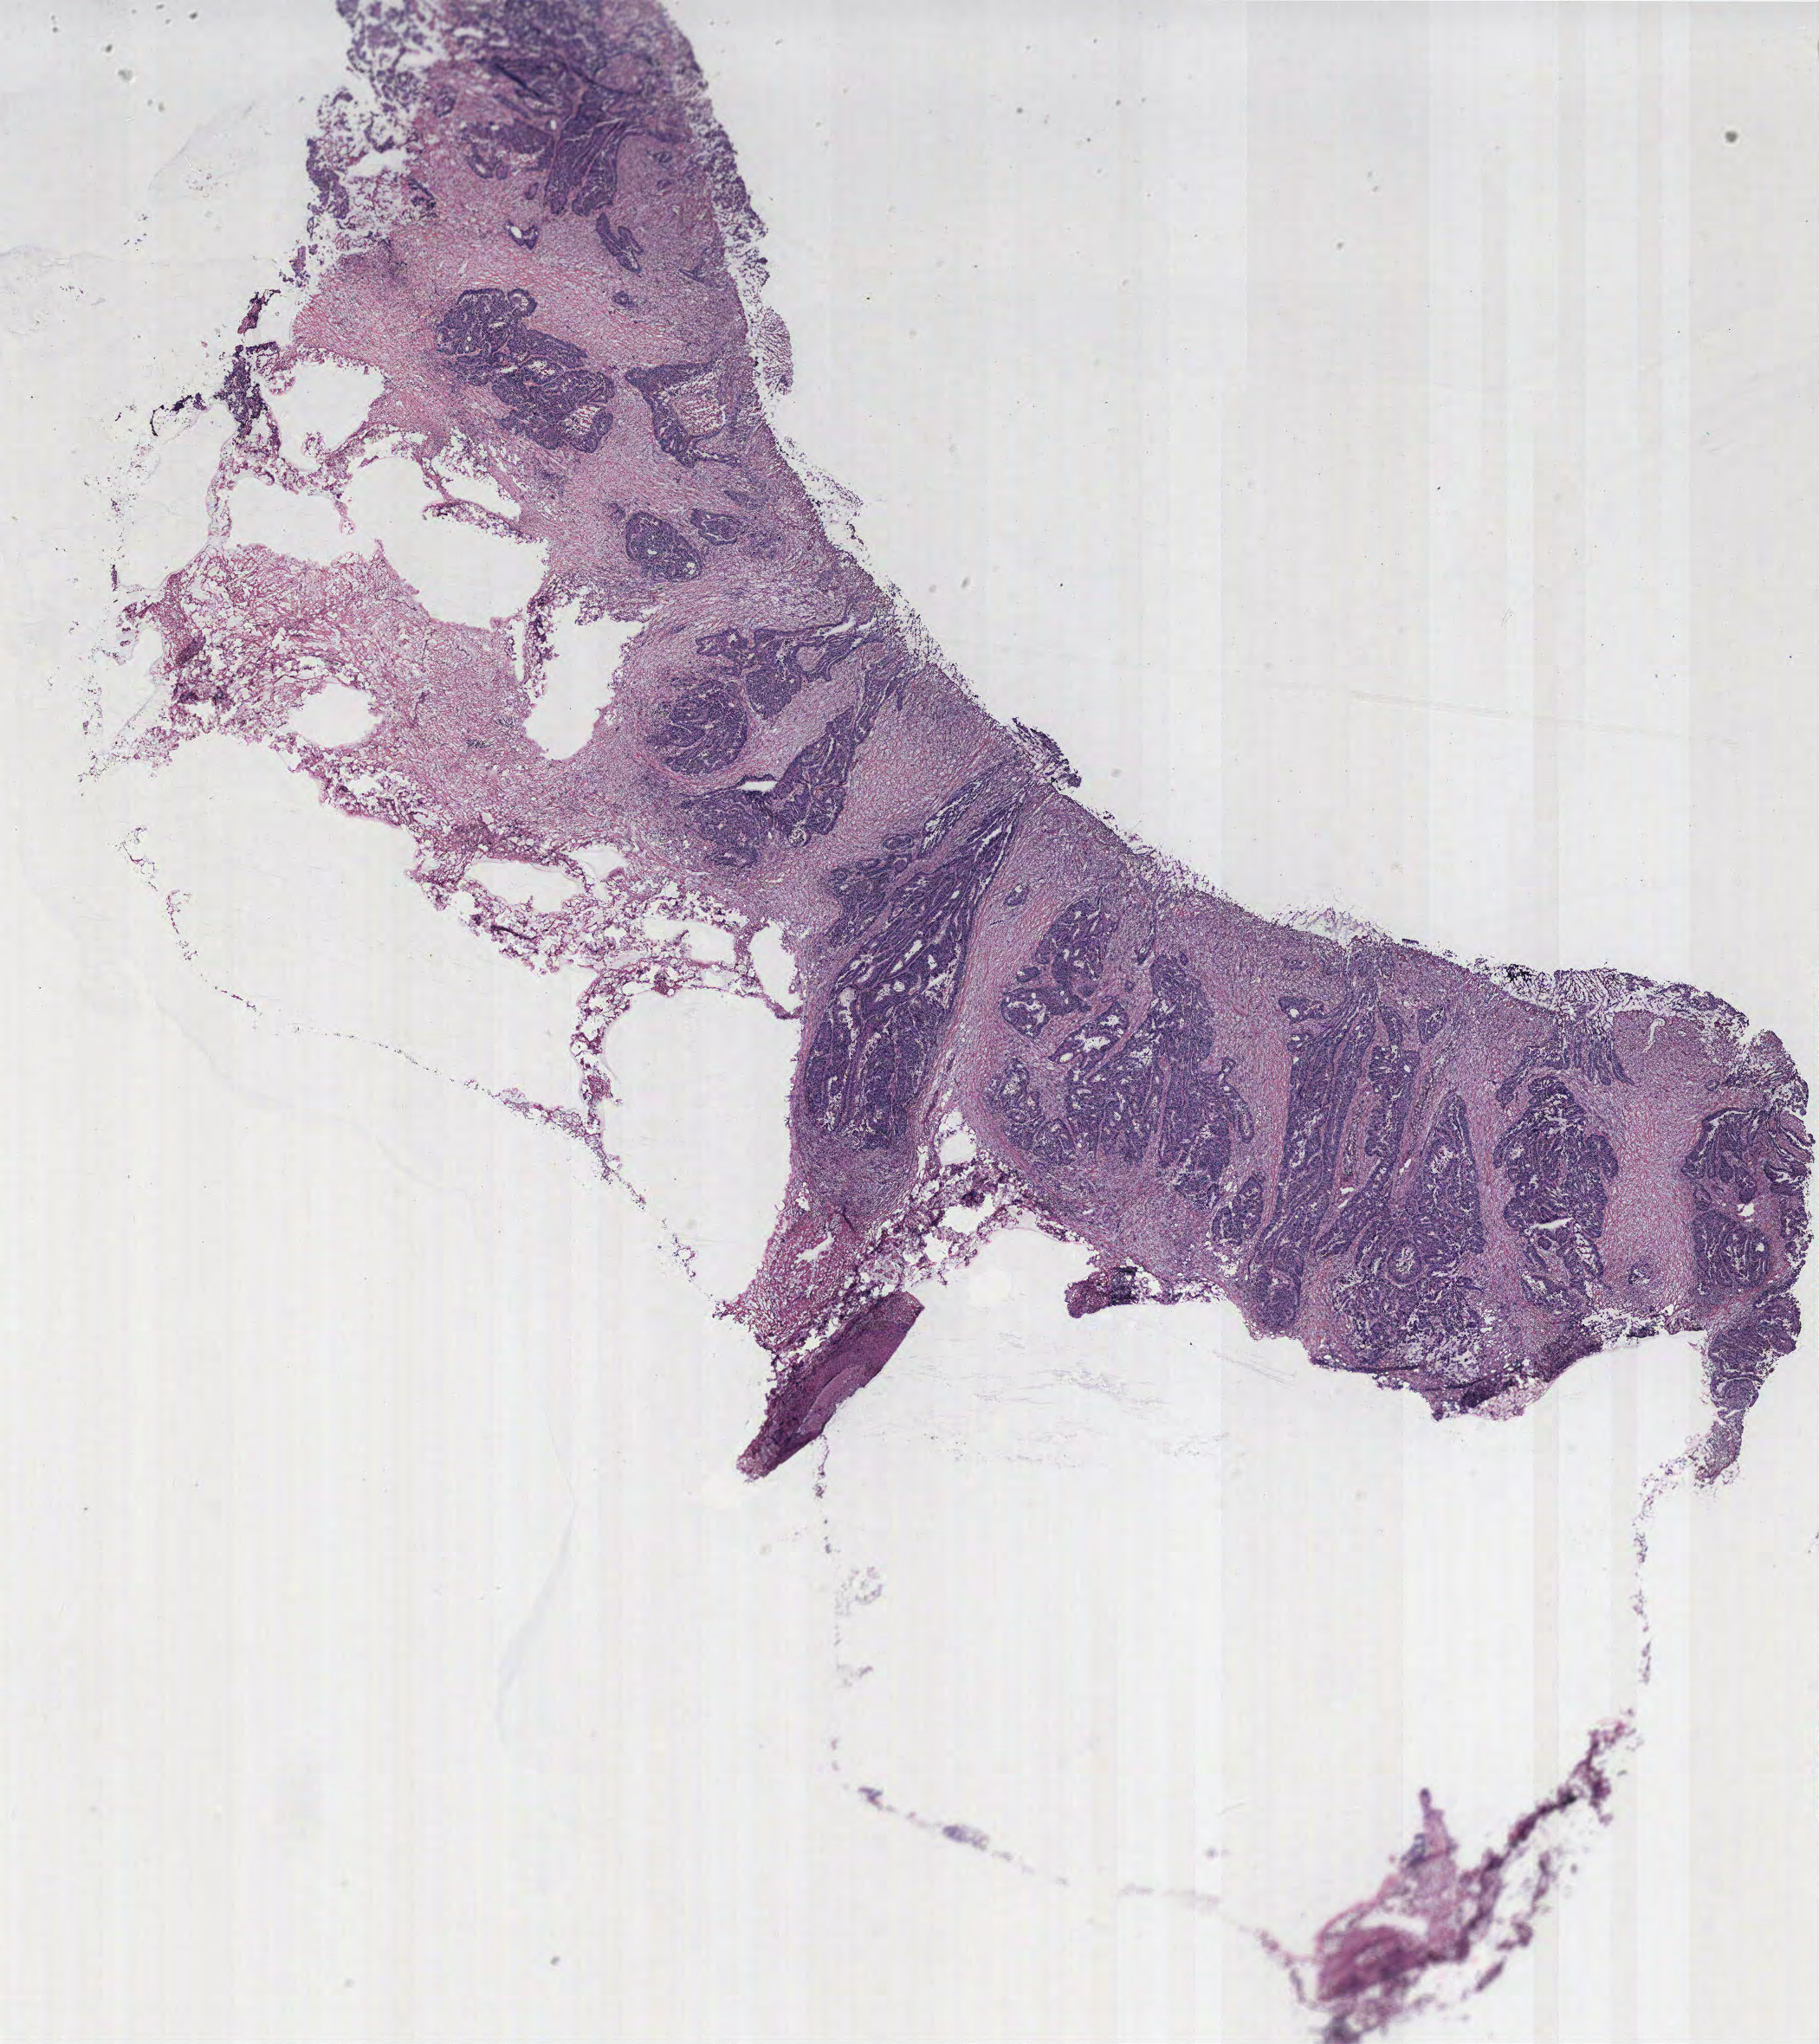
Digitized H&E tissue section (whole slide) — a low-resolution overview of the entire scanned area, about 16.8 x 18.9 mm; tumour tissue sample, colon. Patient: female, age 67 years.
Diagnosis: Adenocarcinoma, NOS.